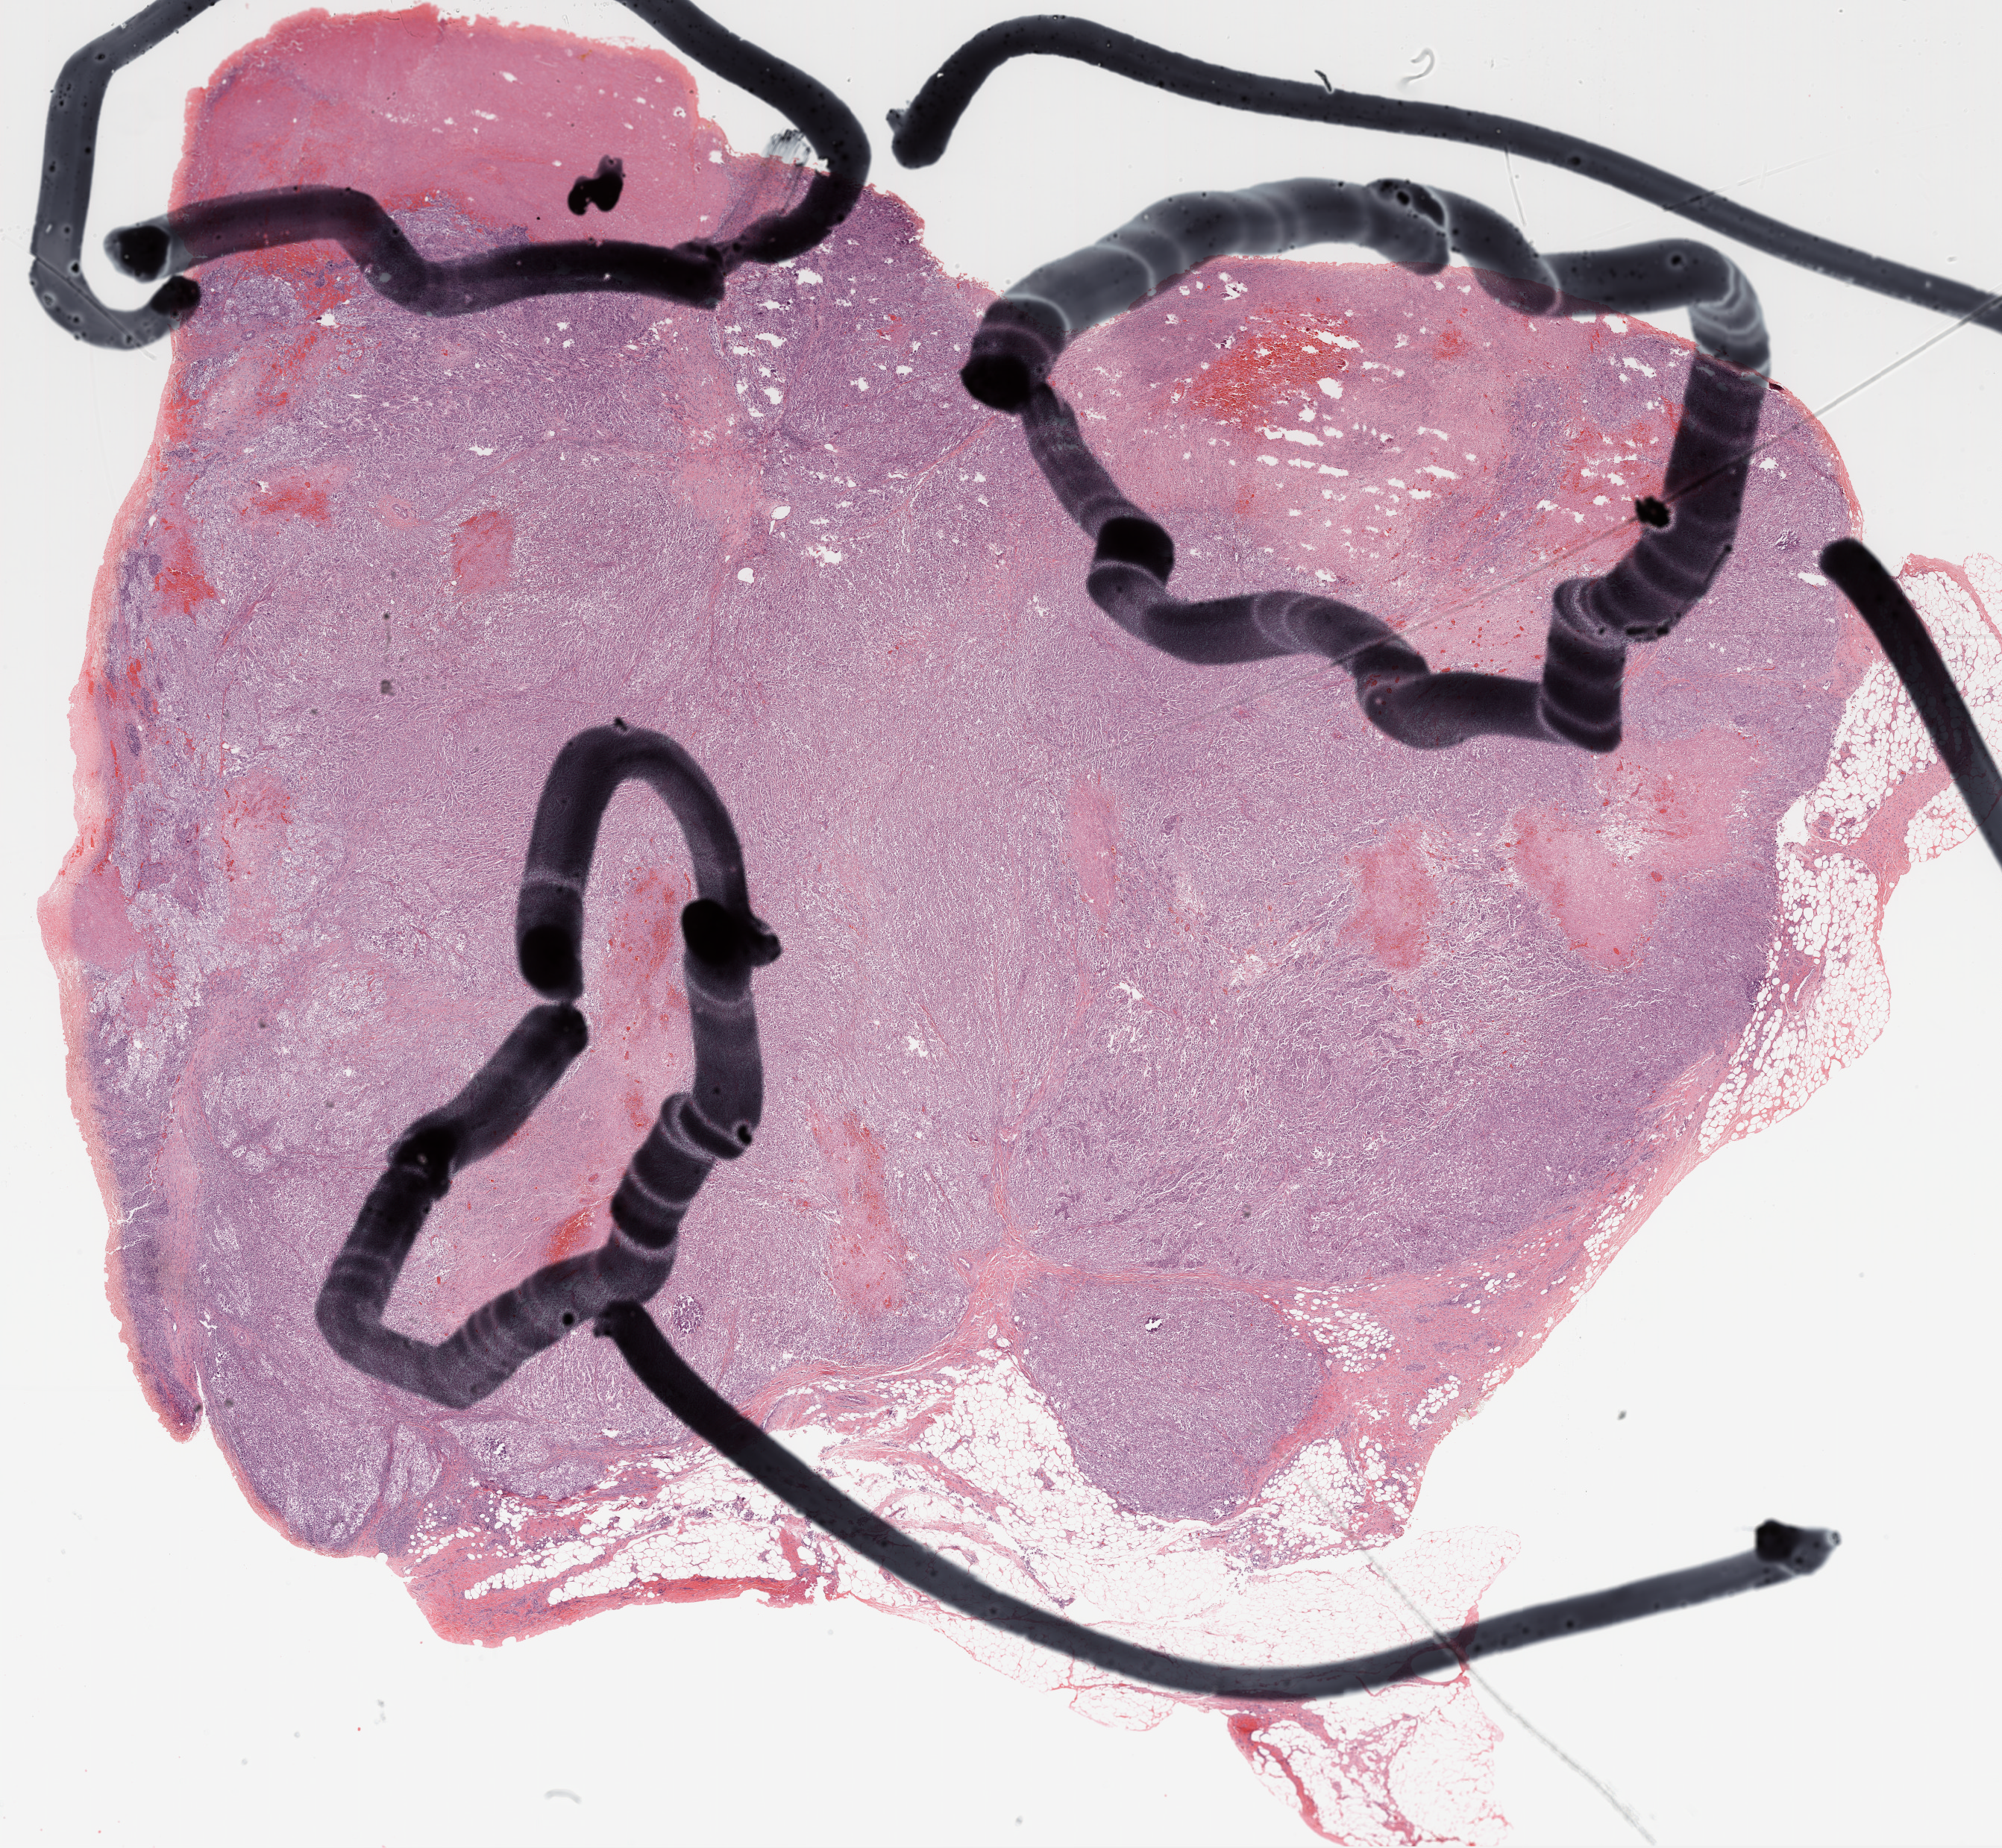
Digitized Hematoxylin and eosin (H&E) stained tissue section (whole slide) — whole scanned area (about 21.6 x 20.0 mm) shown as a low-resolution overview, FFPE section, metastatic tumour sample, sampled site not recorded. Male, age 74 years at initial diagnosis.
* this section: metastatic tumour tissue
* patient diagnosis: Malignant melanoma, NOS